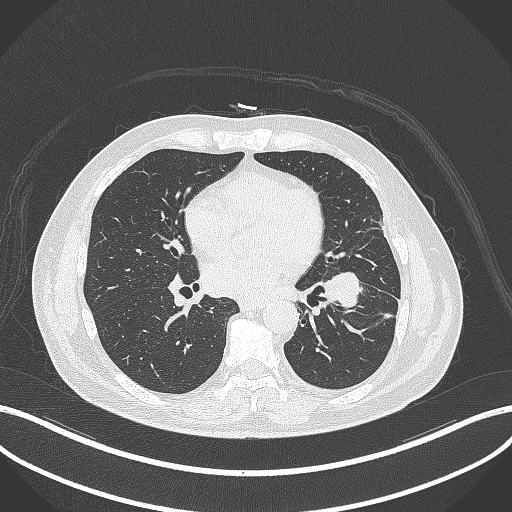
Chest CT, one axial slice; slice 164 of 230 in the series (ordered by position); reconstruction kernel B70f; lung window (W 1500 / L -600 HU); 1 mm slice thickness; 512 × 512 image matrix, field of view 400 × 400 mm. Patient: male, 68 years. Case-level facts recorded for this patient, not image findings: clinical TNM (as recorded): T2b N0 M0.
Outlined on this slice (rectangle marked by the reading radiologist):
- lung tumour (recorded histology: squamous cell carcinoma): bounding box (x1, y1, x2, y2) in pixels: (321, 266, 366, 312)